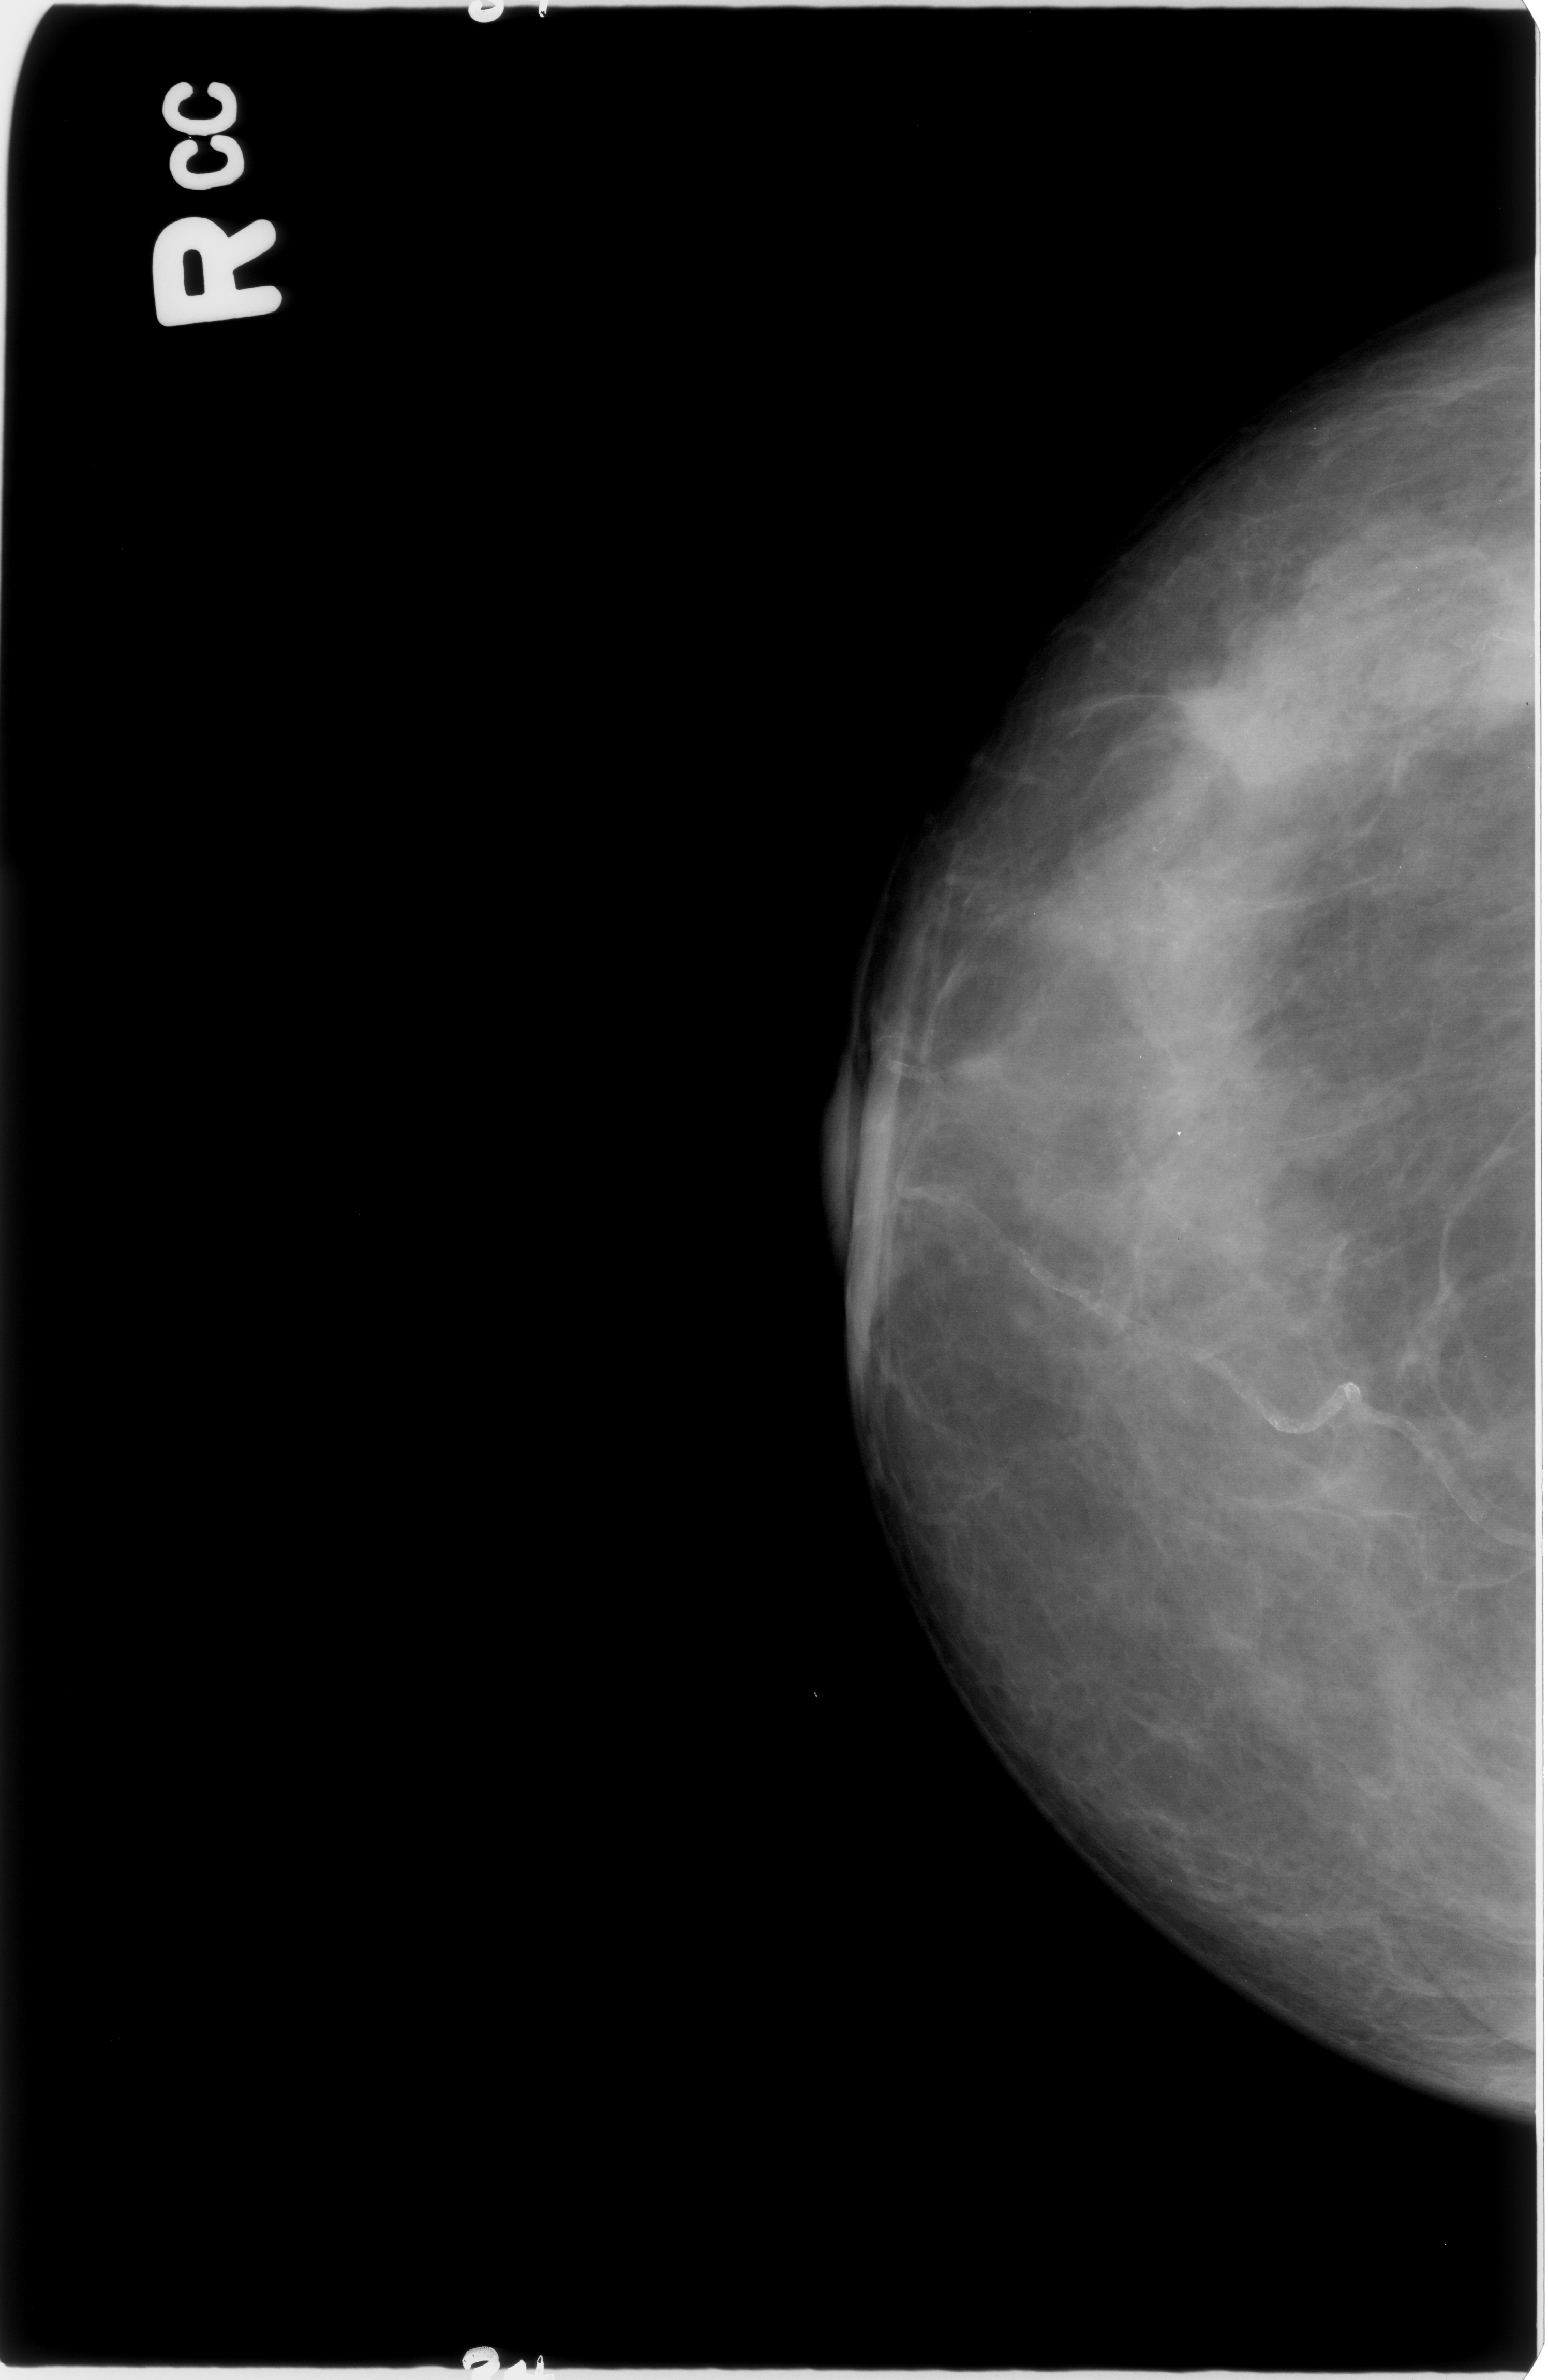
Mammogram (digitized film); right breast; CC view.
- Marked findings (only marked abnormalities are described; nothing is implied about the rest of the image): mass, shape irregular, margins ill defined / spiculated; BI-RADS assessment category 4; subtlety rating 3 on a 1 (subtle) to 5 (obvious) scale; pathology result (as recorded, not read from the image): malignant.